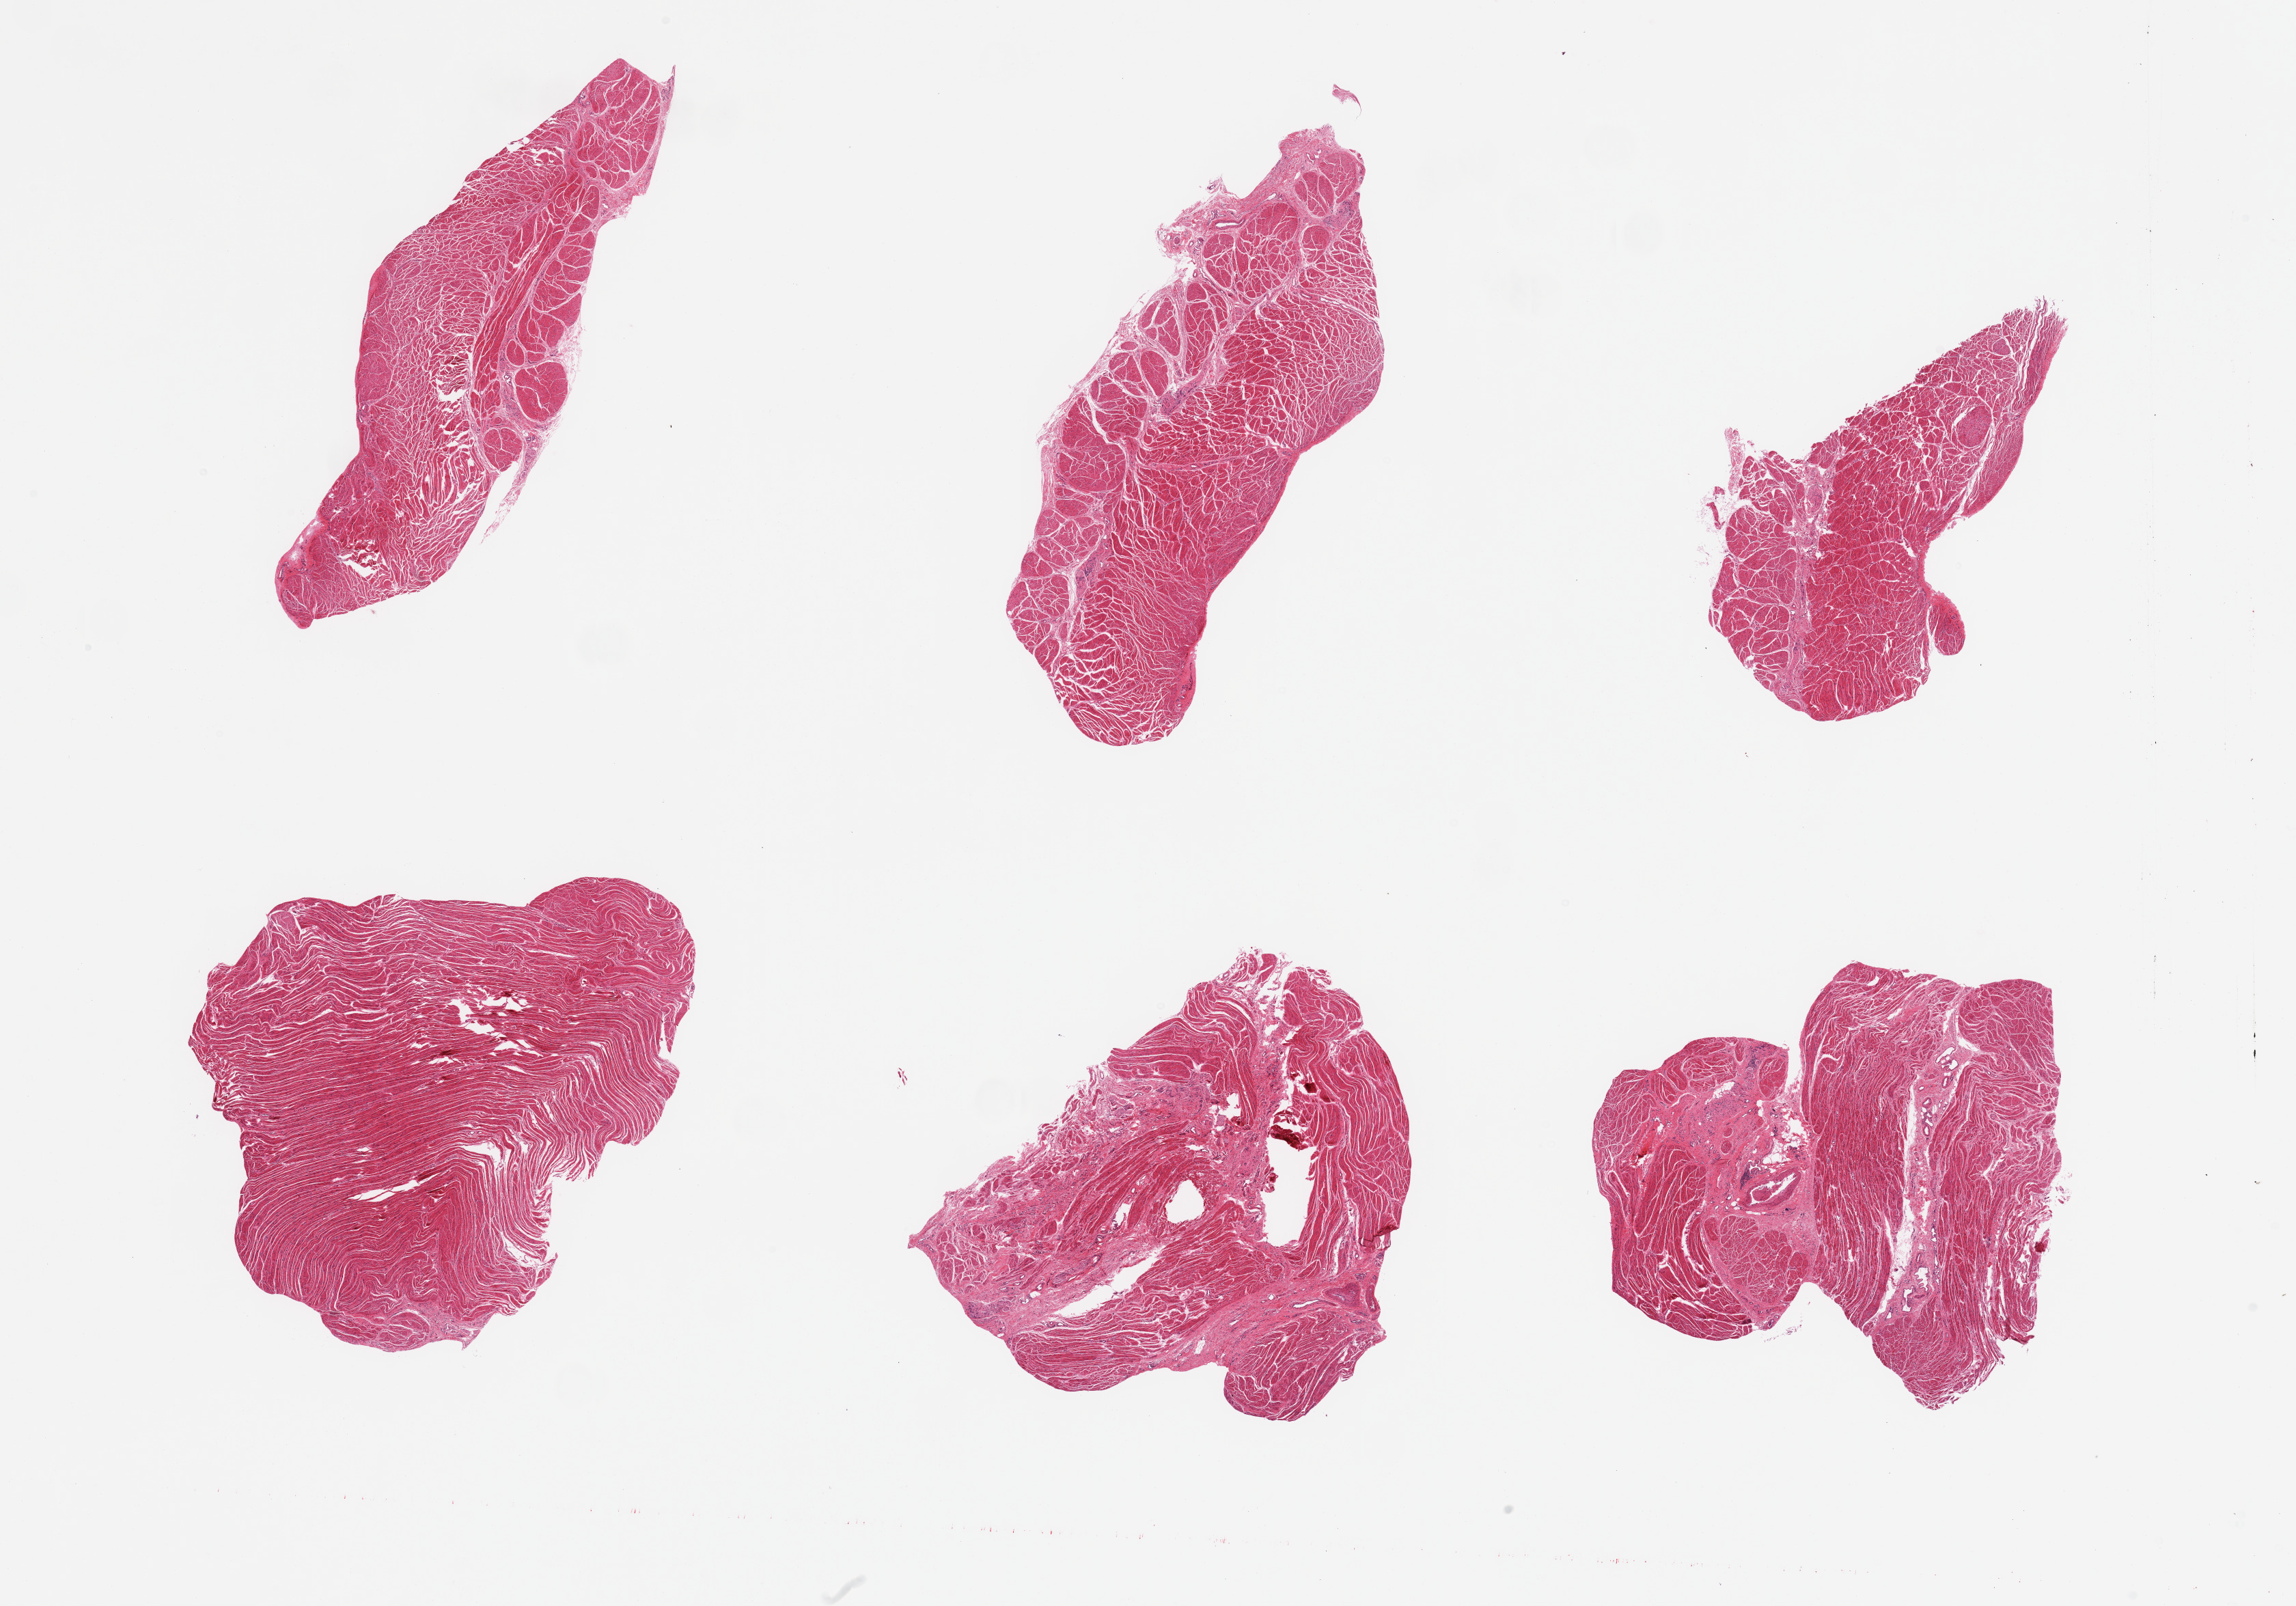
Hematoxylin and eosin (H&E) whole-slide image, low-resolution overview of the scanned area, about 26.6 x 18.6 mm; PAXgene-fixed, paraffin-embedded tissue; target tissue: gastroesophageal junction; donor tissue sample.
* reviewer comment on this tissue sample: 6 pieces, confirmed target muscularis